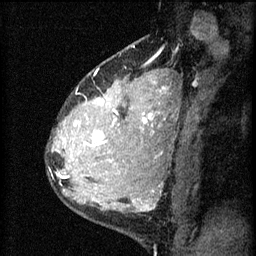
Breast MRI (dynamic contrast-enhanced), one sagittal slice; slice 43 of 60 in the series (ordered by position); 3 images stored at this slice position (order not interpretable as contrast timing); 1.5 T; TE 4.2 ms, TR 8.2 ms; 2 mm slice thickness; 256 × 256 image matrix, field of view 180 × 180 mm. Patient: female, 37 years.
Annotated regions visible in this slice (semi-automatically segmented with operator editing):
- analysis volume of interest (the breast-tissue region the enhancement analysis was run in; not a lesion): bounding box <53,78,140,181> (left, top, right, bottom; pixels)
- tumour enhancement mask (voxels above the 70 % enhancement threshold inside the analysis volume of interest): <58,110,119,177>